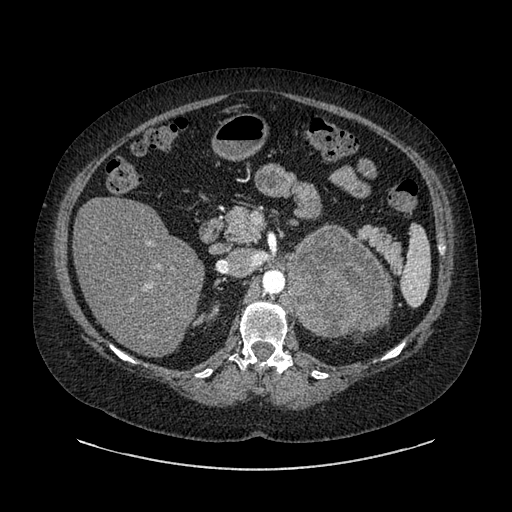
Contrast-enhanced abdominal CT, one axial slice. Slice 556 of 769 in the series (ordered by position). Intravenous contrast given. Soft-tissue window (W 400 / L 40 HU). 0.62 mm slice thickness. 512 × 512 image matrix, field of view 460 × 460 mm. Patient: female, 61 years. Case-level facts recorded for this patient, not image findings: diagnosis: adrenocortical carcinoma; tumour side: left adrenal; tumour size at pathology: 13 cm; Ki-67 index: 79 %; stage (as recorded): 2.
Structures marked on this image (semi-automatically segmented with operator editing):
- mass: bounding box <289,229,390,335> (left, top, right, bottom; pixels)